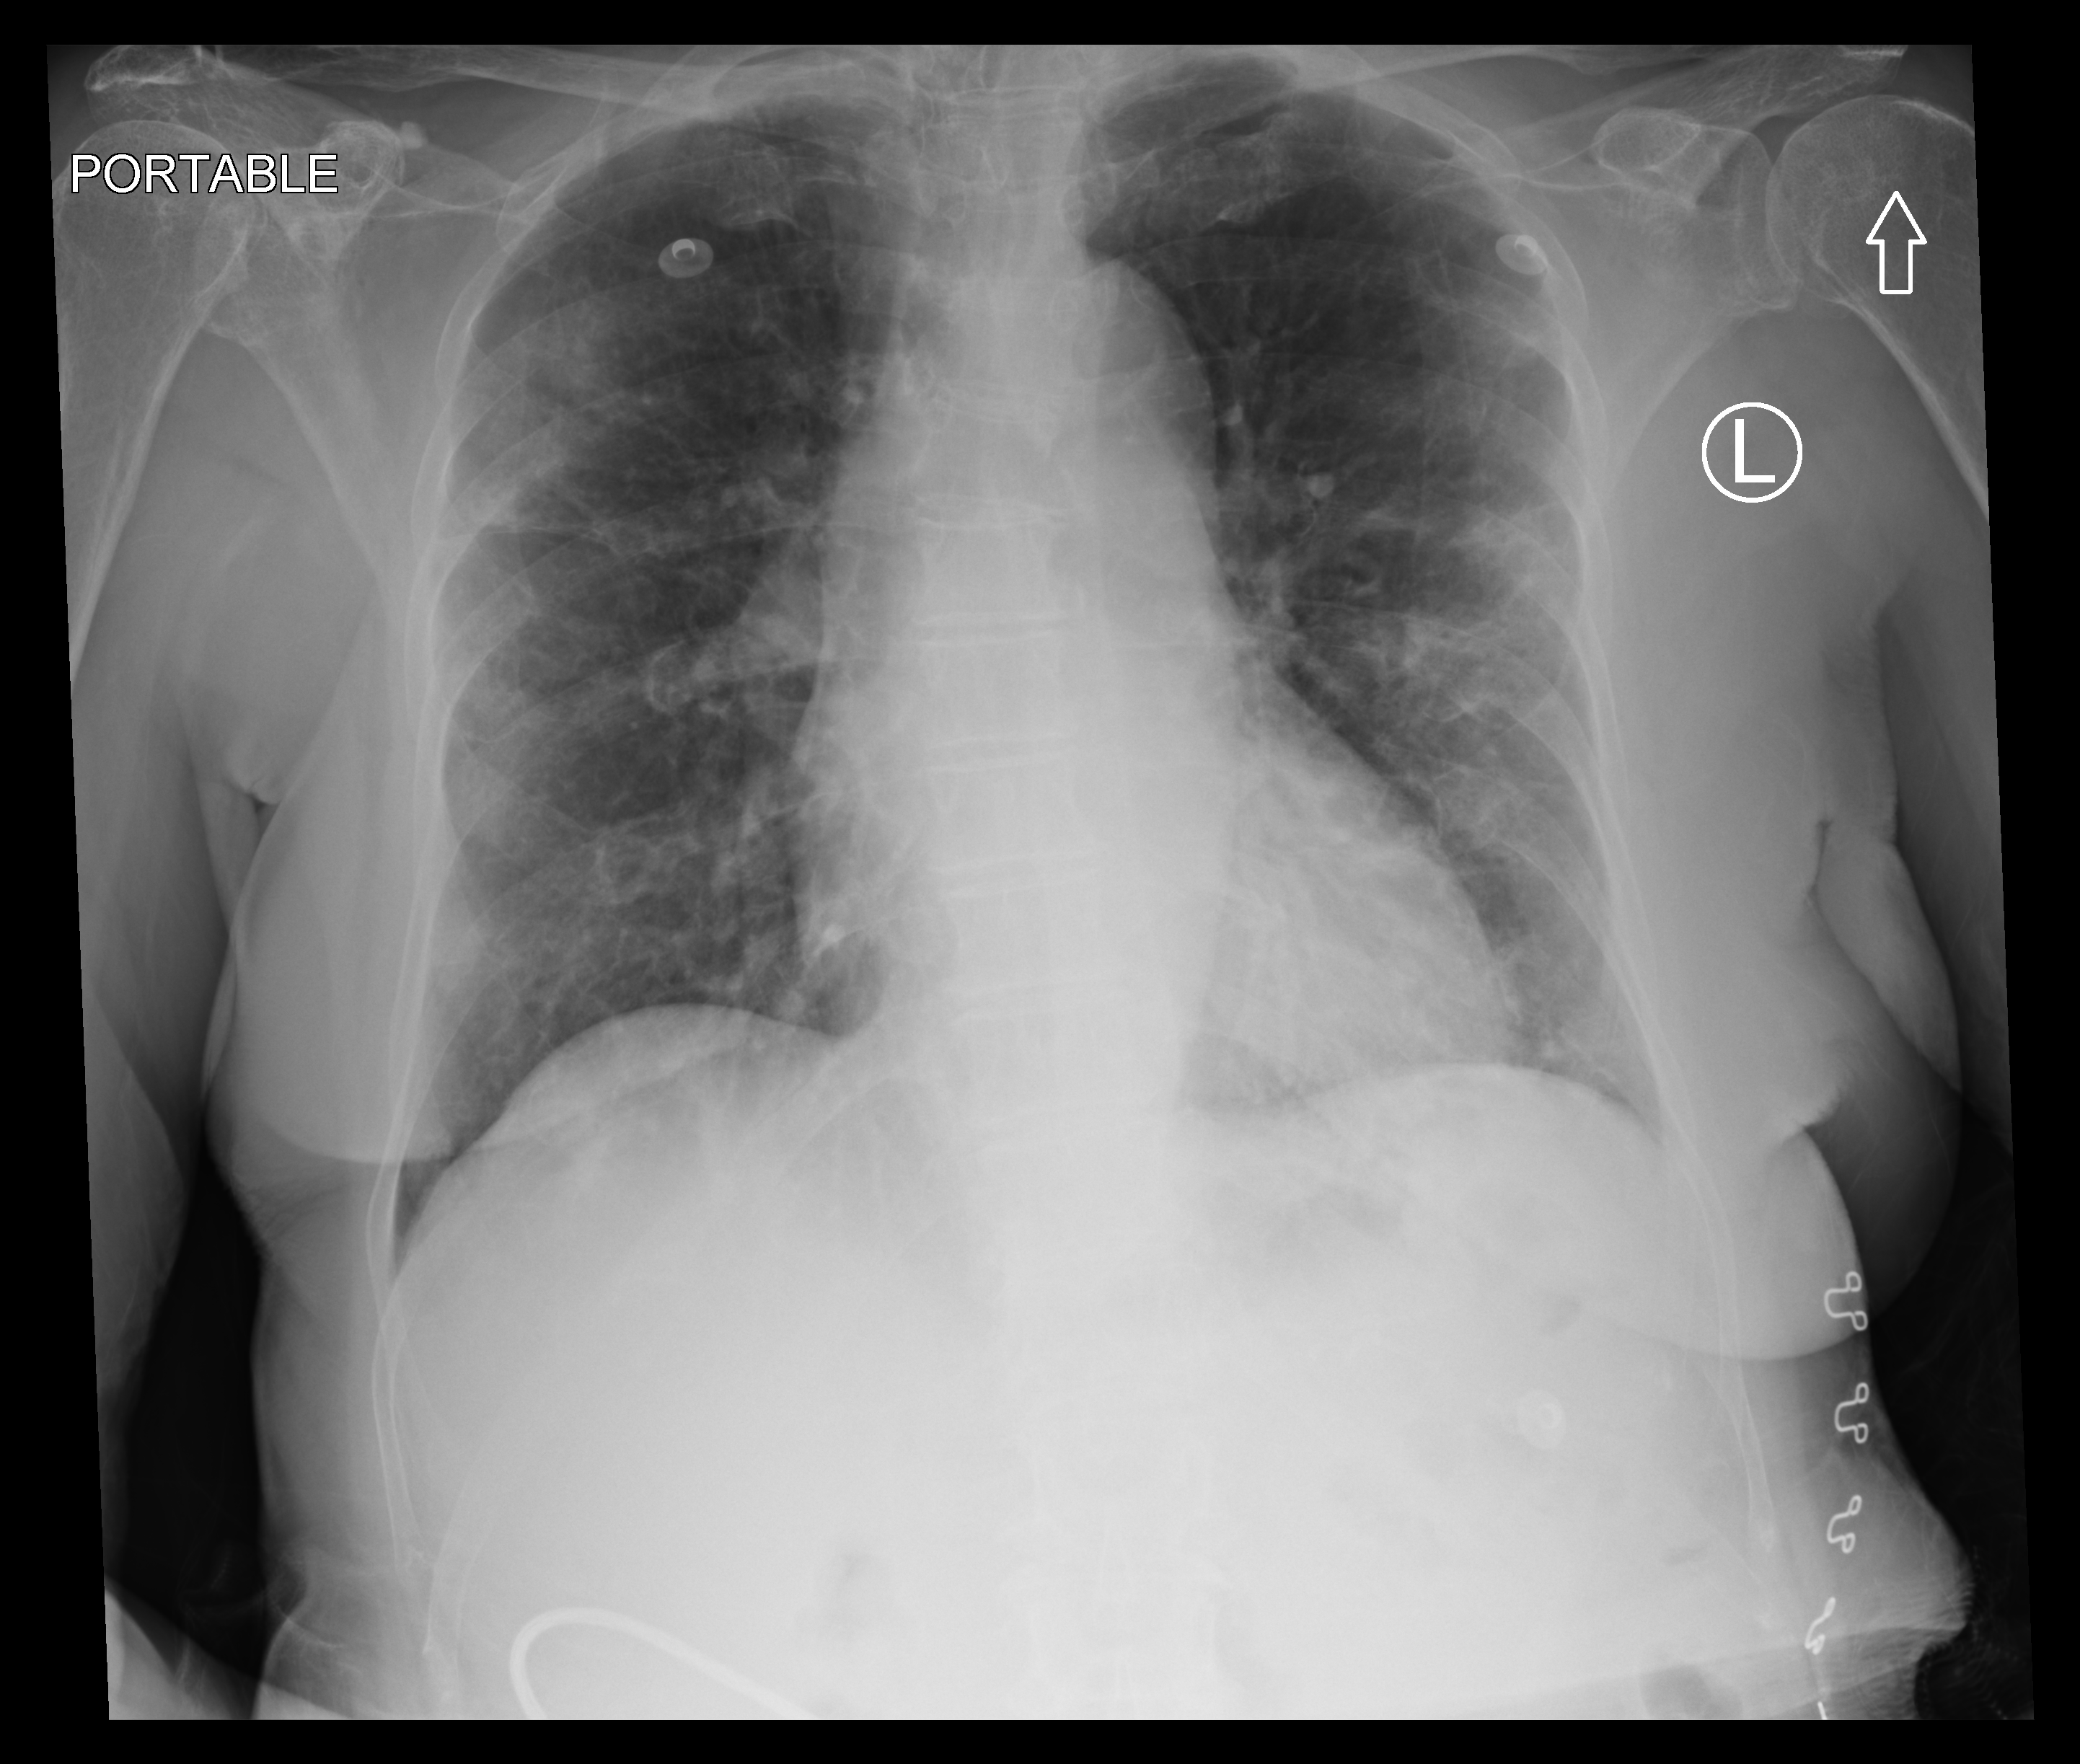
Chest X-ray (portable), anteroposterior (AP) projection. Female patient hospitalised with COVID-19, age 75–90 years.
From the hospital-stay record, not from the radiograph (when in the stay this image was taken is not recorded):
- mechanically ventilated during this hospital stay: no
- diabetes (admission record): no